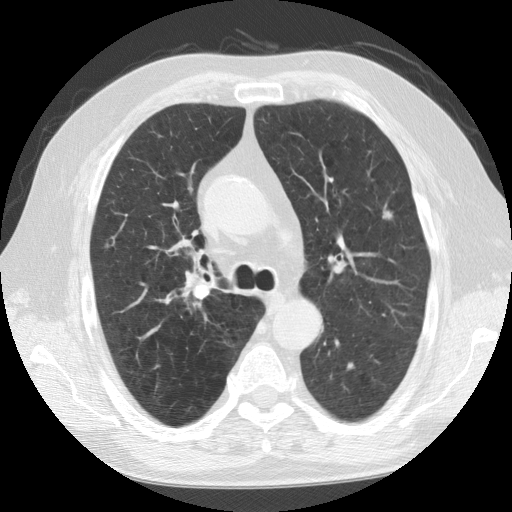
Chest CT (low-dose screening protocol), one axial image. Second annual screen. Lung window (W 1500 / L -600 HU). 2.5 mm slice thickness. Standard (soft-tissue) reconstruction kernel (STANDARD). 120 kVp. 512 × 512 image matrix. Male, age 64 years at enrolment.
Expert reader's lesion annotation, bounding box (x1, y1, x2, y2) in pixels: (369, 201, 405, 235). The screening reader recorded 2 non-calcified nodules or masses ≥4 mm on this exam; which of them this box marks is not recorded. Later outcome: lung cancer diagnosed 233 days after this screen — squamous cell carcinoma, NOS, left upper lobe, moderately differentiated (G2), stage IA (AJCC 6th edition), 10 mm at pathology.